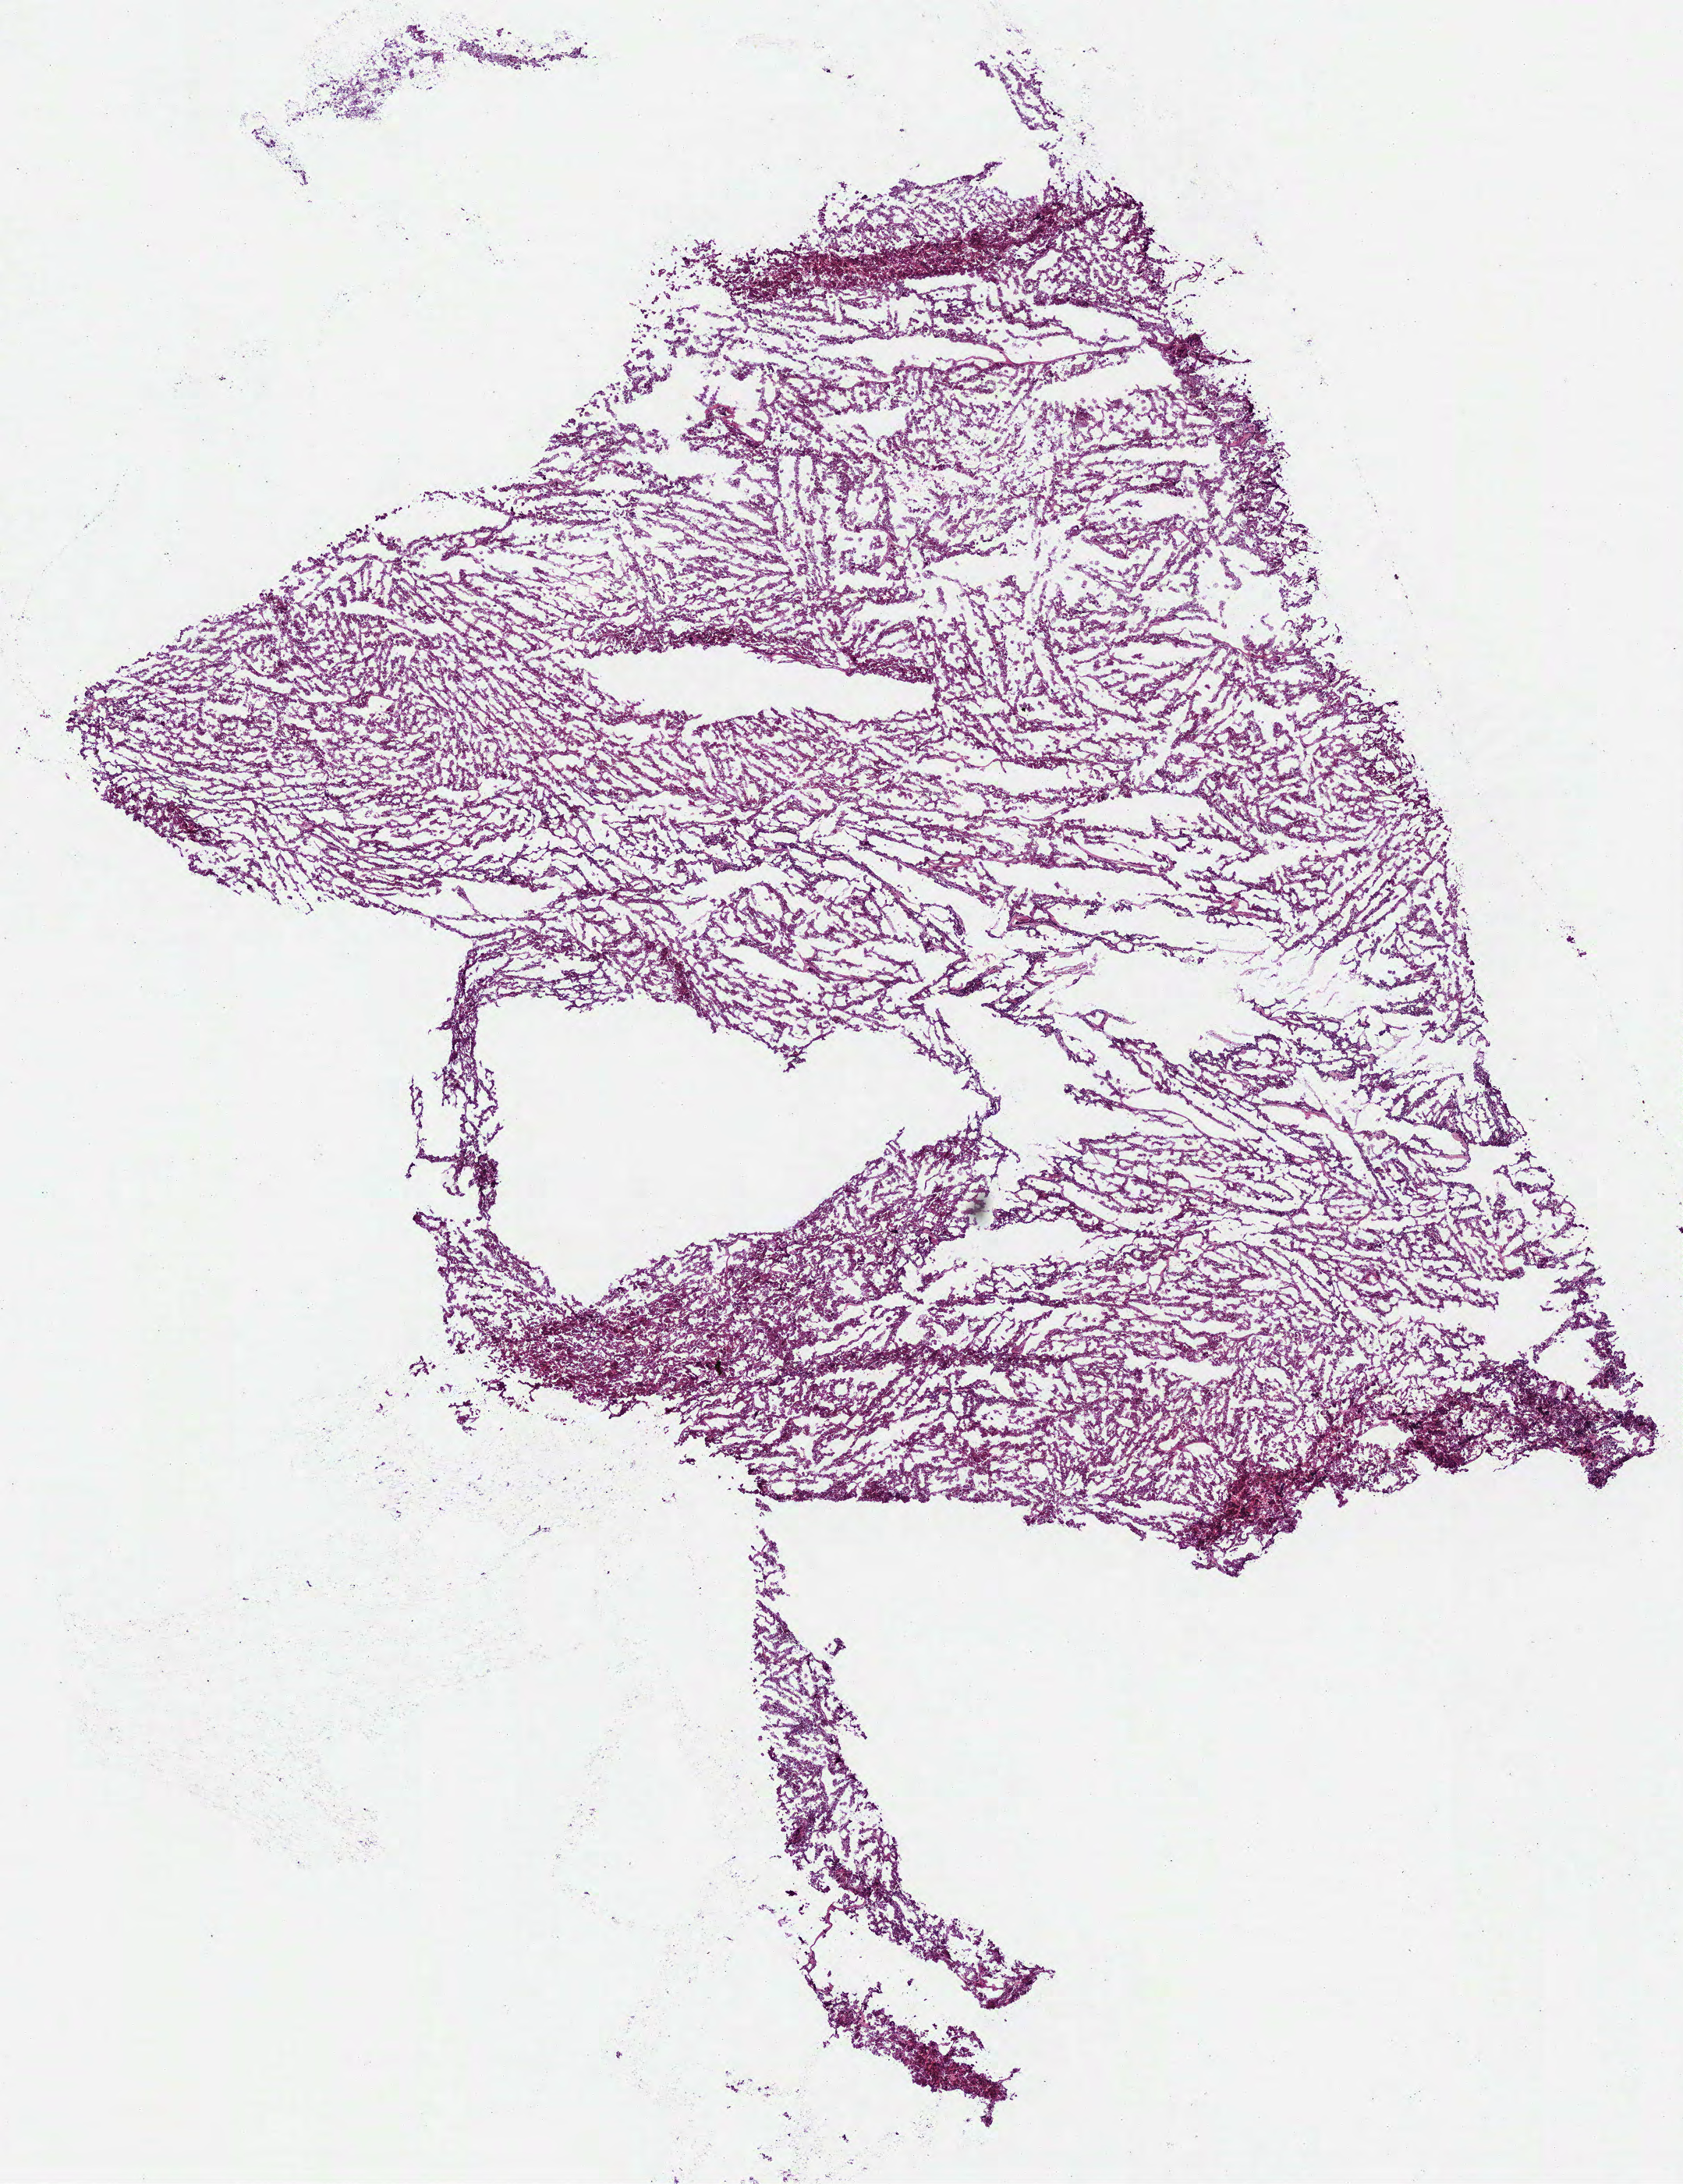
H&E-stained whole-slide image, low-resolution overview of the scanned area, about 8.7 x 11.3 mm; frozen section from the bottom of the tissue portion; primary tumour sample from the kidney. Female patient; age at initial diagnosis 47 years. Pathologist review of this section (percent, as recorded): tumour cells 100%, tumour nuclei 90%, normal cells 0%, stromal cells 0%, necrosis 0%. Inflammatory infiltration, as recorded: lymphocyte infiltration 0%, monocyte infiltration 0%, neutrophil infiltration 0%.
Diagnosis: Renal cell carcinoma, chromophobe type. Laterality: left. AJCC pathologic stage: II (6th edition). Lymph nodes positive (case pathology): 0 of 2 examined. TNM: T2 N0.